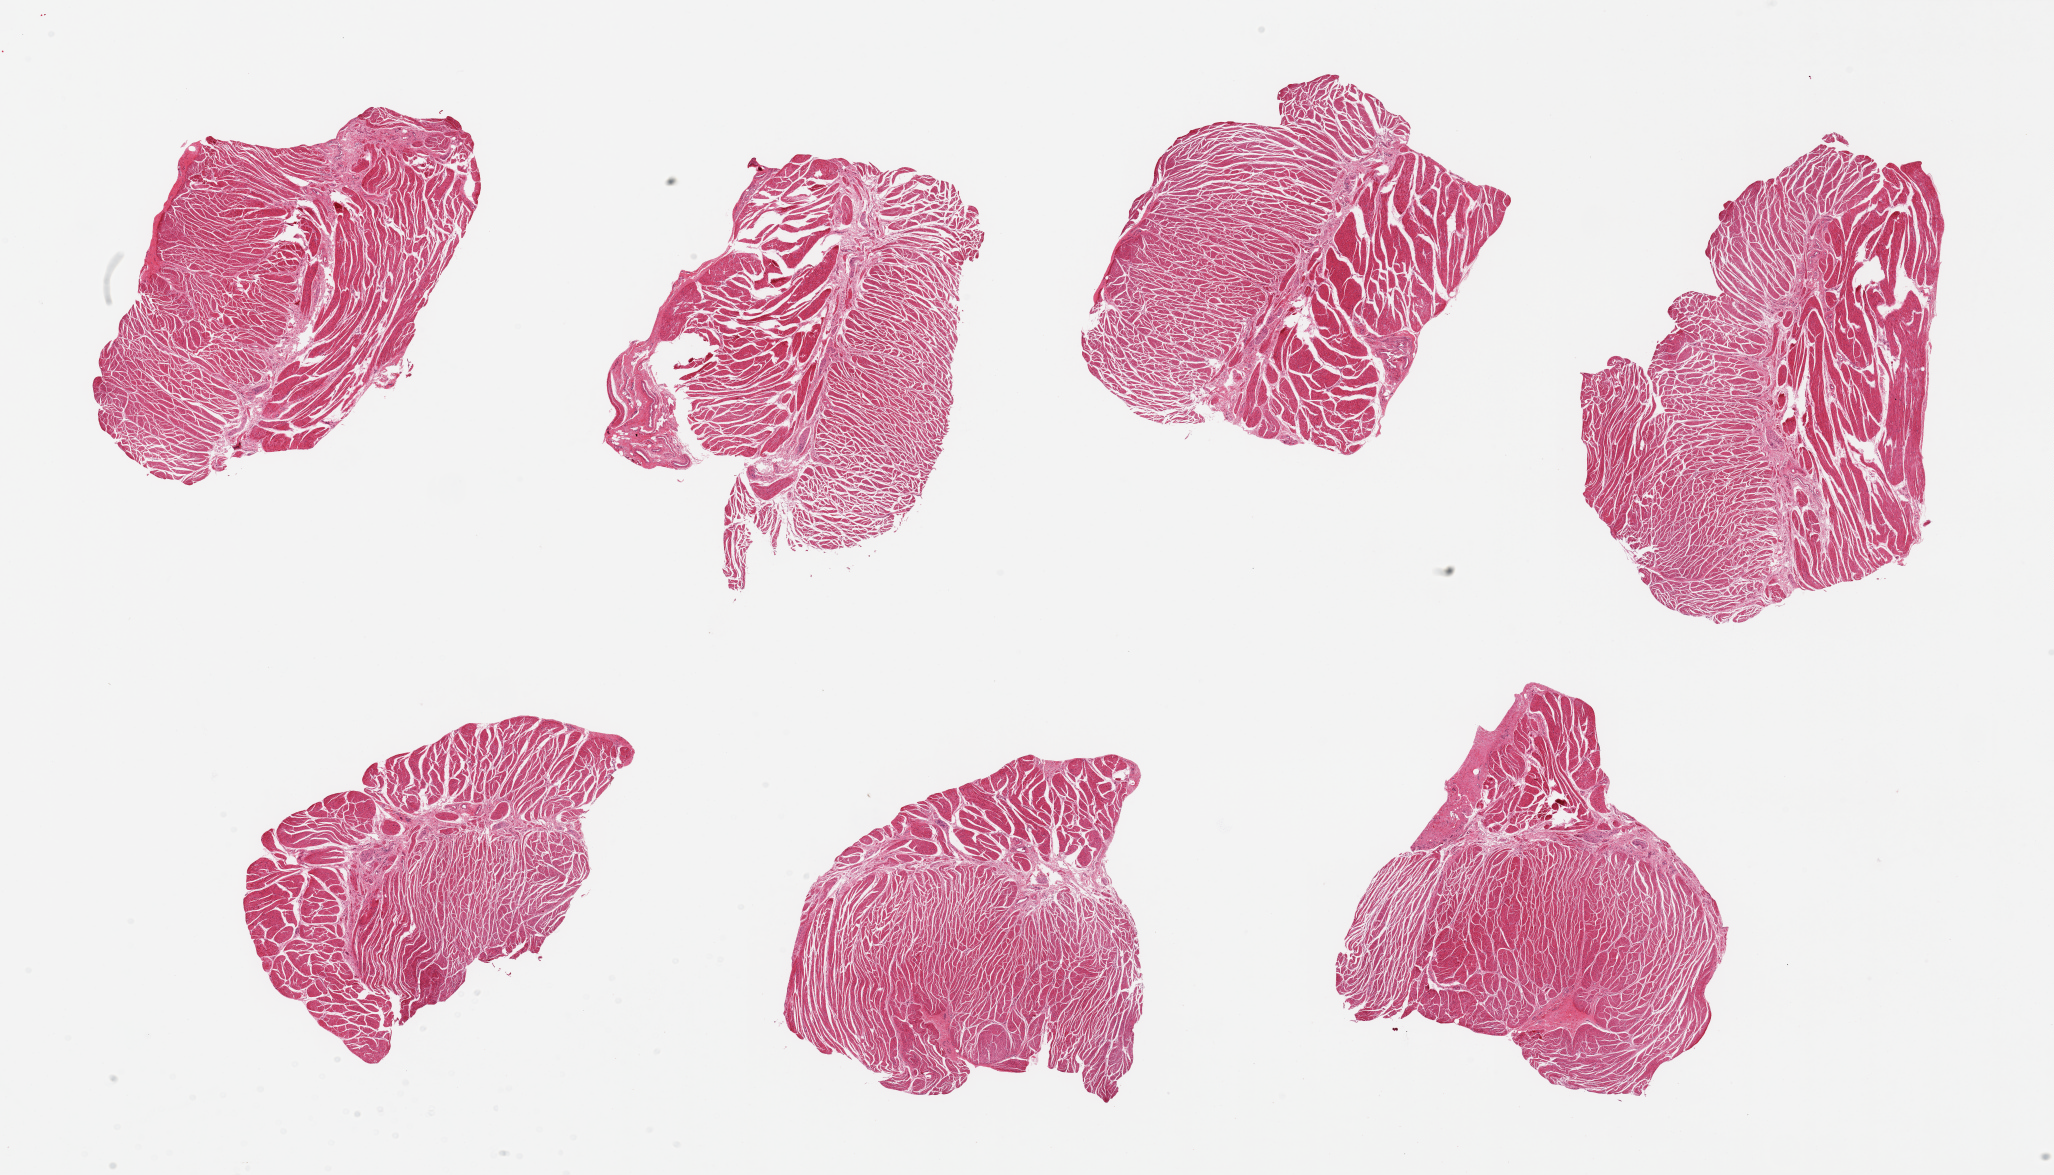
Digitized H&E-stained section, brightfield, a low-resolution overview of the entire scanned area, about 32.5 x 18.6 mm. PAXgene-fixed, paraffin-embedded tissue. Section of esophageal muscle (target tissue). Tissue donor sample. Male donor.
Pathologist's review note for this sample: 7 pieces ~8x4mm.